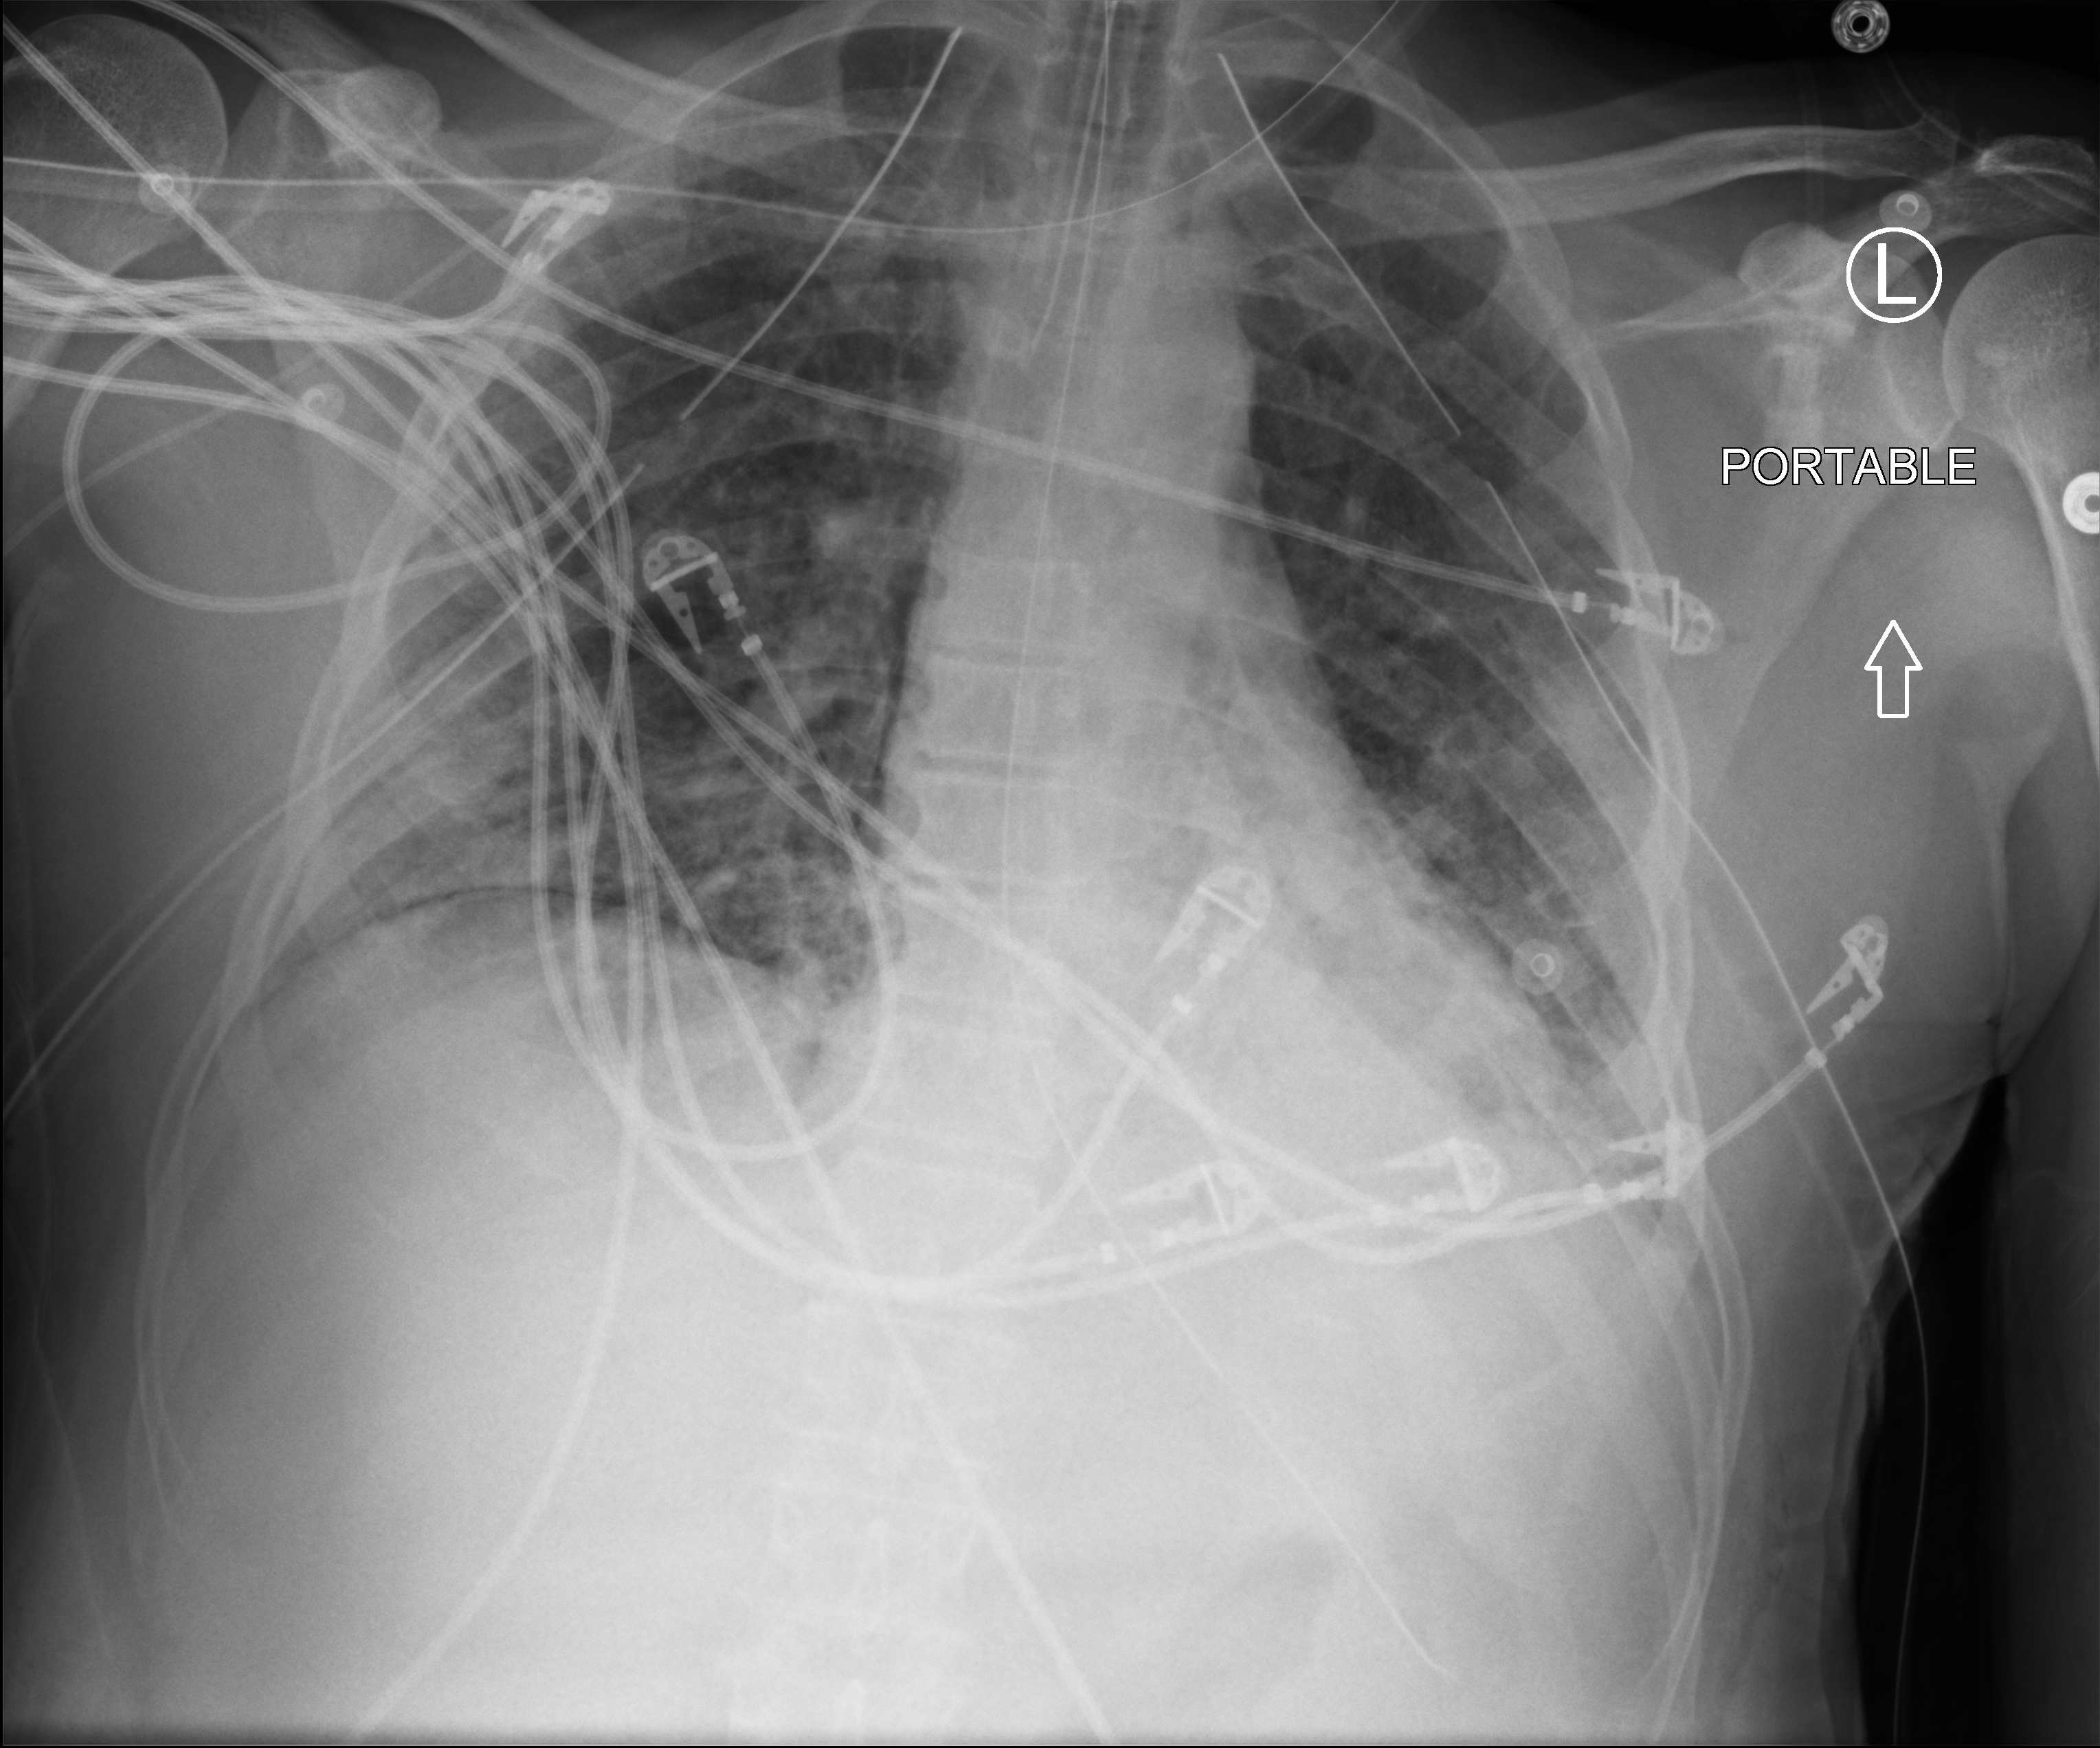
Bedside chest radiograph (computed radiography), anteroposterior (AP) projection. Male patient hospitalised with COVID-19, age 18–59 years.
From the hospital-stay record, not from the radiograph (when in the stay this image was taken is not recorded): admitted to intensive care during this hospital stay: yes; length of hospital stay: 83 days.